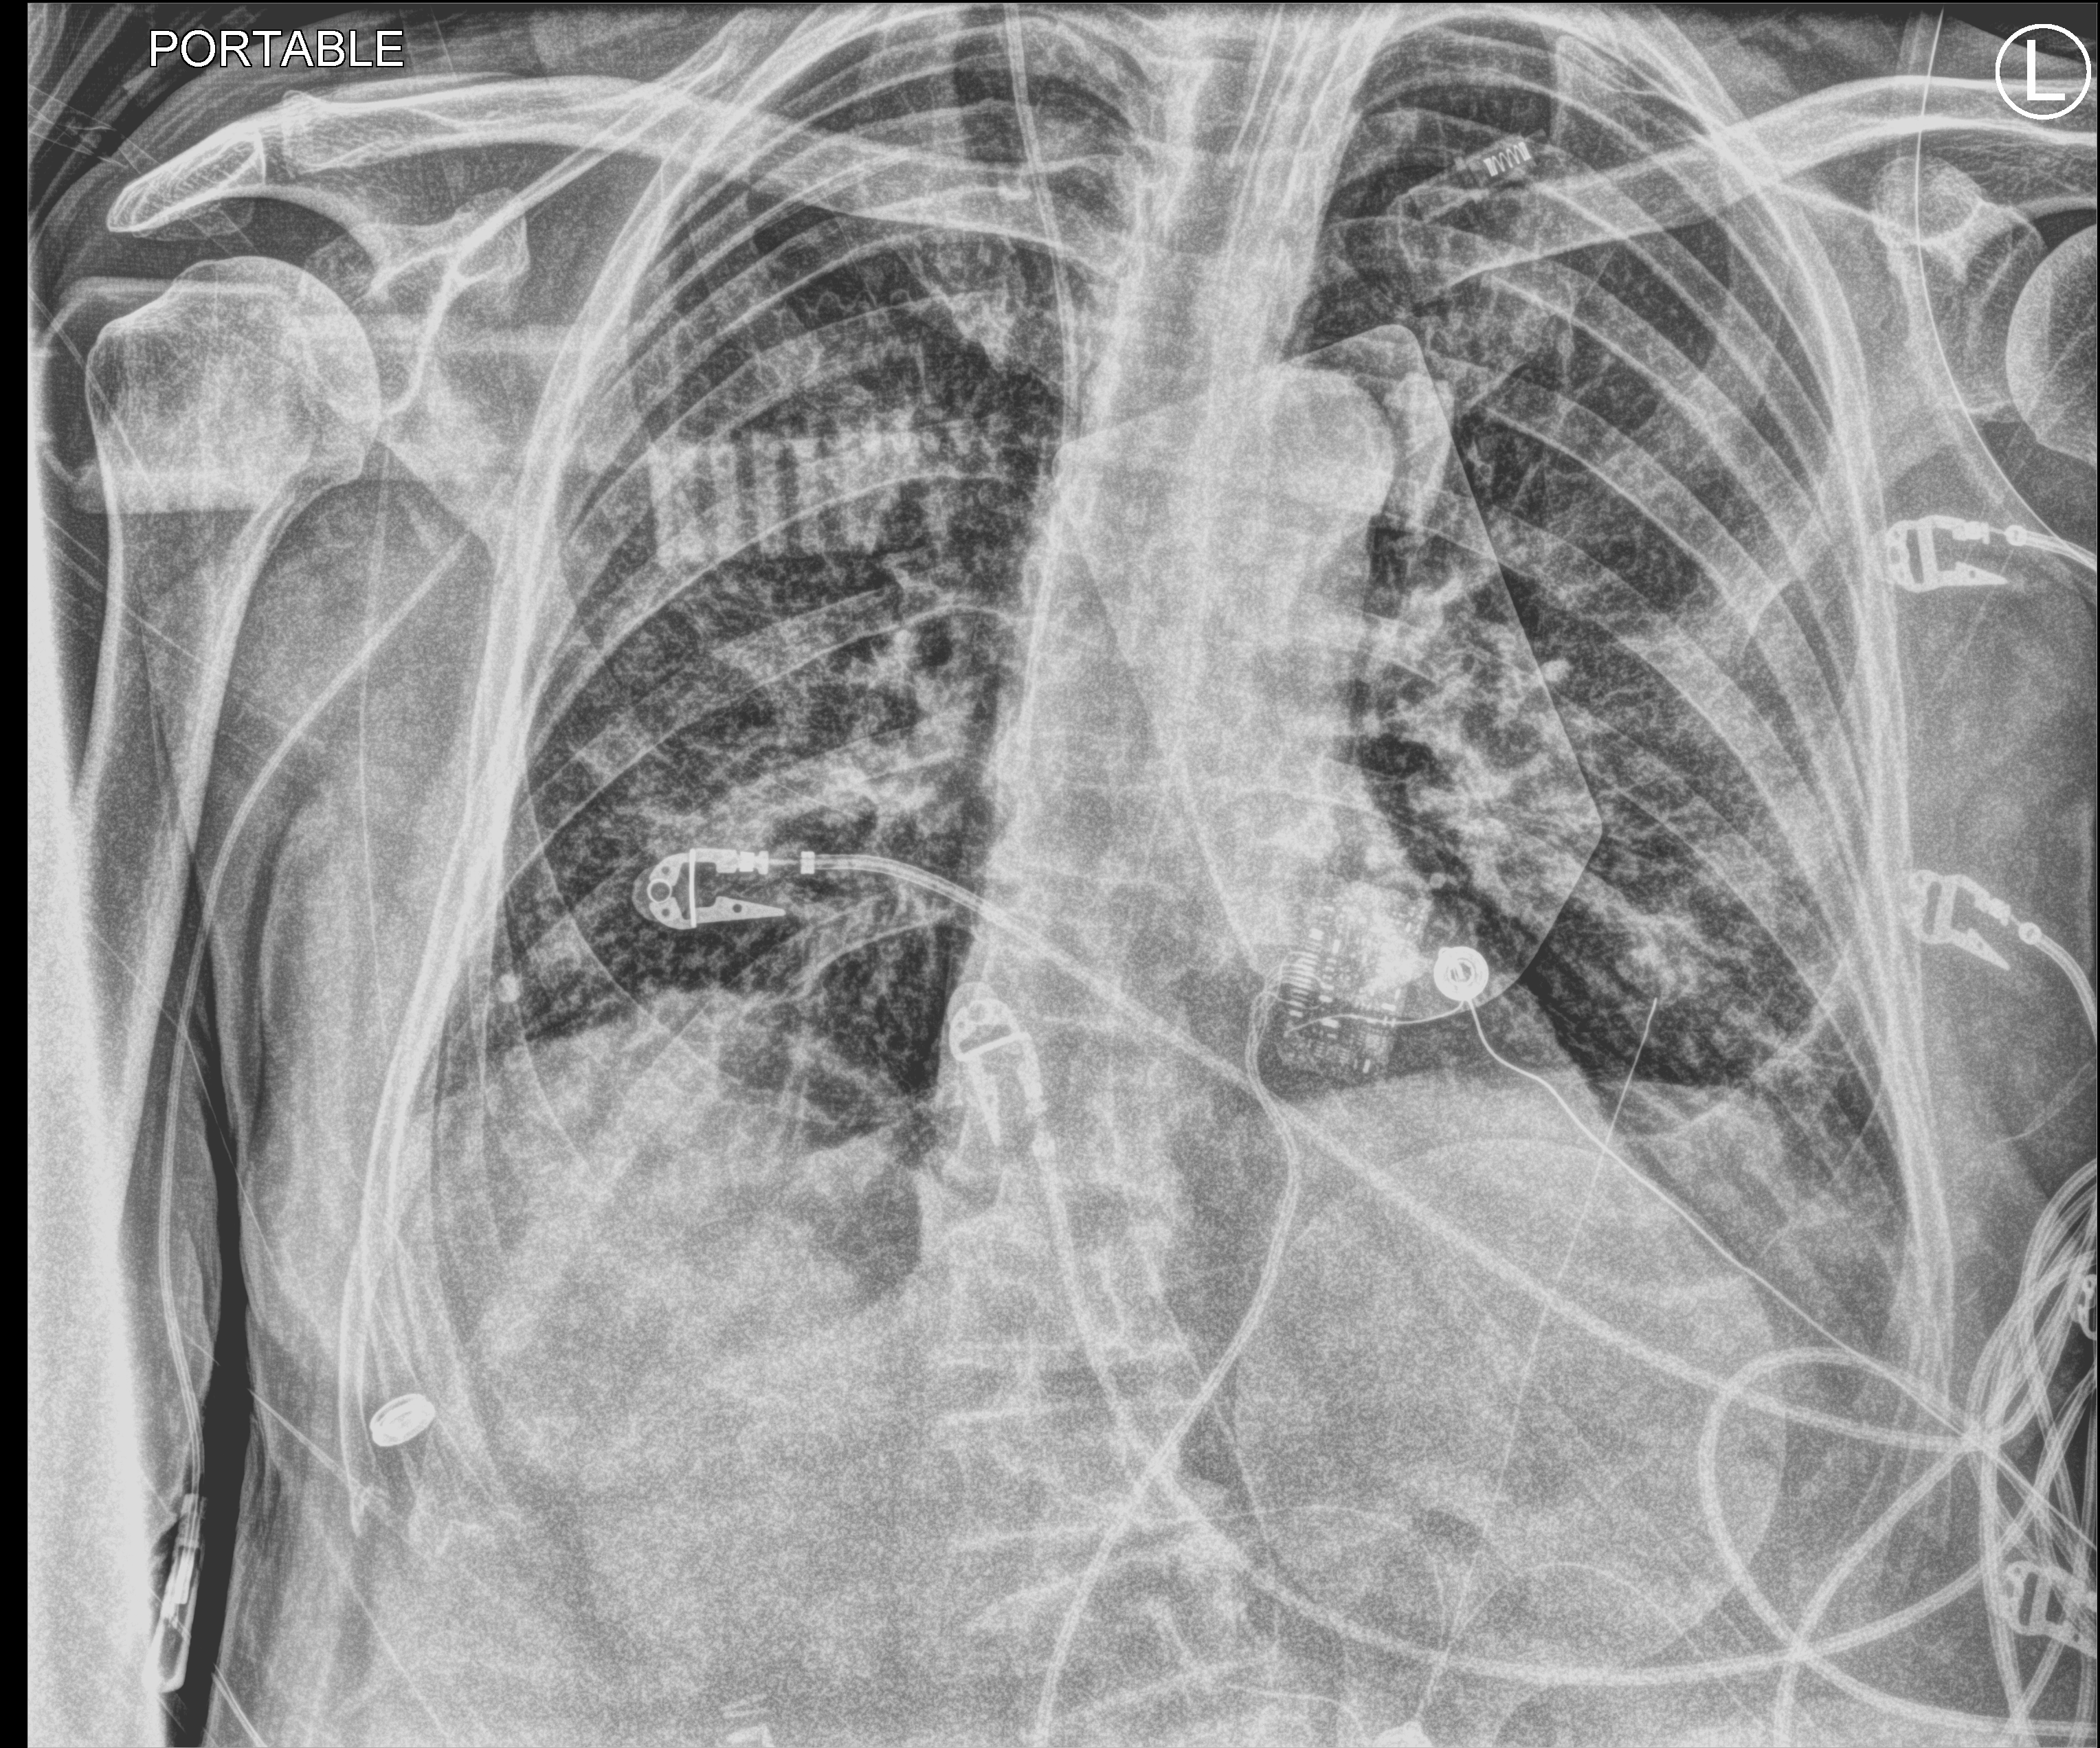
Portable chest radiograph. Patient hospitalised with COVID-19; male, aged 75–90 years.
Admission-level facts for this patient (not findings on this image; timing relative to this image not recorded):
- admitted to intensive care during this hospital stay: yes